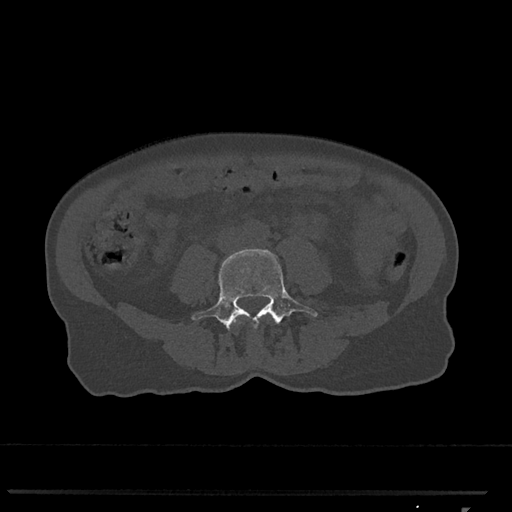
CT including the spine, one axial slice. Slice 221 of 793 in the series (ordered by position). 120 kVp. Bone window (W 1800 / L 400 HU). 512 × 512 image matrix. Patient: female, 62 years. Case-level facts recorded for this patient, not image findings: primary cancer: renal.
Outlined on this slice (semi-automatically segmented with operator editing):
- L3 vertebra: box from (x=234, y=318) to (x=241, y=325) px
- L4 vertebra: (x=192, y=249)–(x=318, y=330)